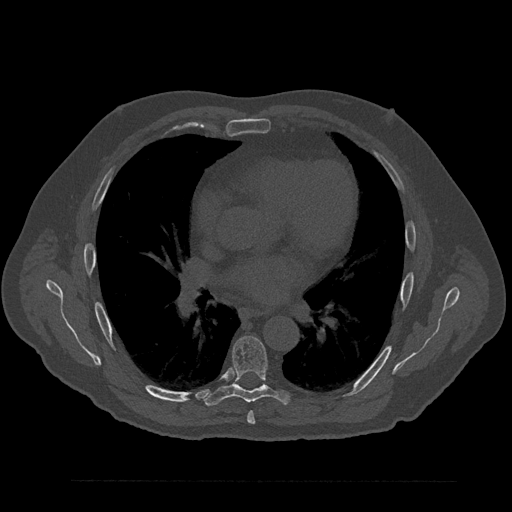
CT including the spine, one axial slice. Position 512 of 797 along the scan axis. Reconstruction kernel Br40s/3. Bone window (W 1800 / L 400 HU). 0.5 mm slice thickness. 512 × 512 image matrix, field of view 430 × 430 mm. Male patient, age 61 years. Case-level facts recorded for this patient, not image findings: primary cancer: prostate.
Annotated regions visible in this slice (semi-automatically segmented with operator editing):
- T6 vertebra: bounding box (x1, y1, x2, y2) in pixels: (247, 411, 255, 424)
- T7 vertebra: (204, 336, 291, 406)